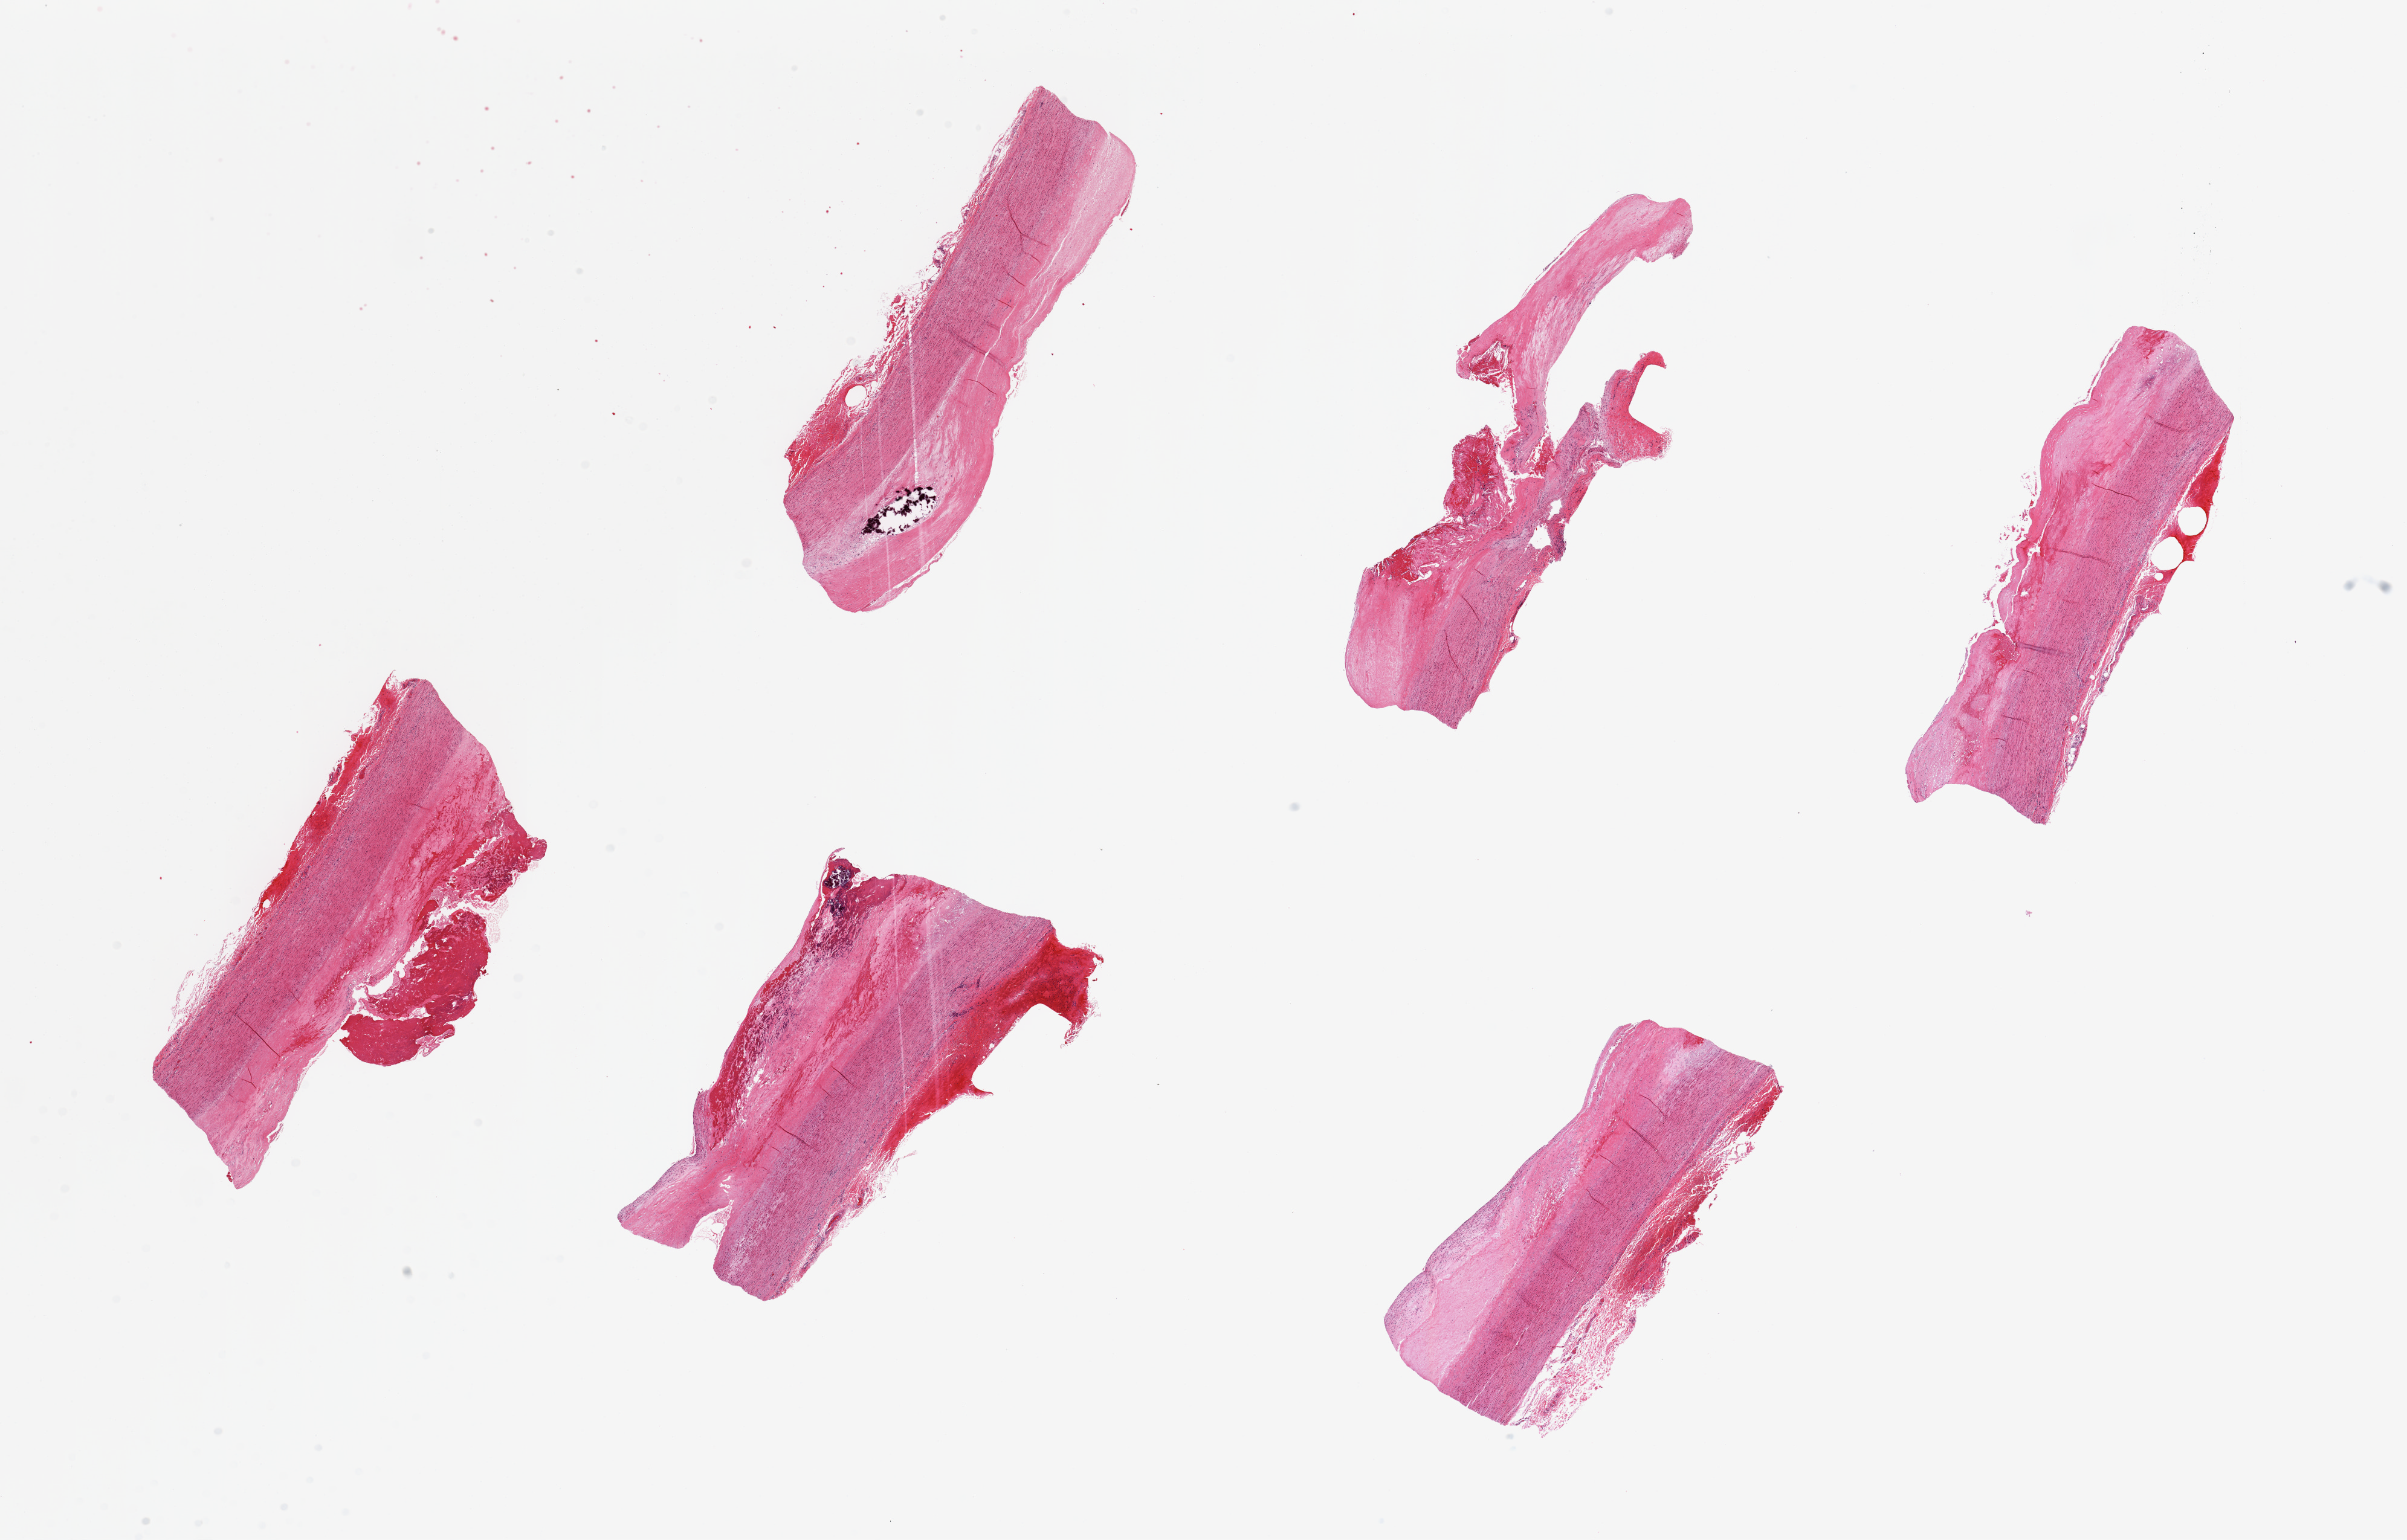
Hematoxylin and eosin (H&E) whole-slide image, brightfield, a low-resolution overview of the entire scanned area, about 31.5 x 20.2 mm (from a 20x scan). PAXgene-fixed paraffin-embedded (PFPE) section. Section of aorta (target tissue). Donor tissue sample. Donor sex: female.
Review note (as recorded): 6 pieces, up to 8x3mm; Severe atherosclerosis with calcium; periaortic hemorrhage (aneurysm repair-clin history). Only media has normal tissue.